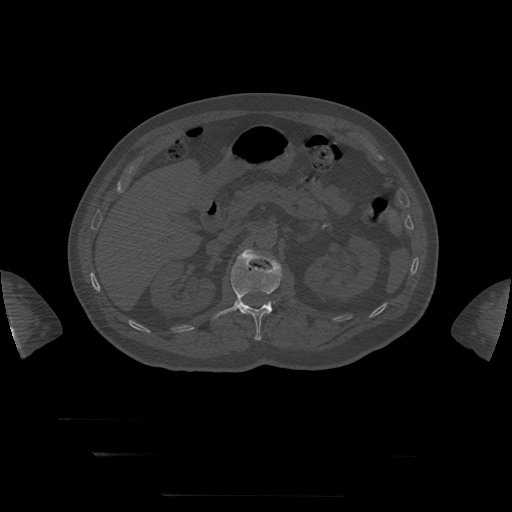
CT including the spine, one axial slice. Slice 45 of 397 in the series (ordered by position). Reconstruction kernel STANDARD. 120 kVp. Bone window (W 1800 / L 400 HU). 1.25 mm slice thickness. 512 × 512 image matrix, field of view 510 × 510 mm. Patient age 73 years. From the clinical record (not read from this slice): primary cancer: prostate.
Outlined on this slice (semi-automatic segmentation, software-assisted and operator-edited):
- L1 vertebra: box from (x=212, y=249) to (x=282, y=341) px